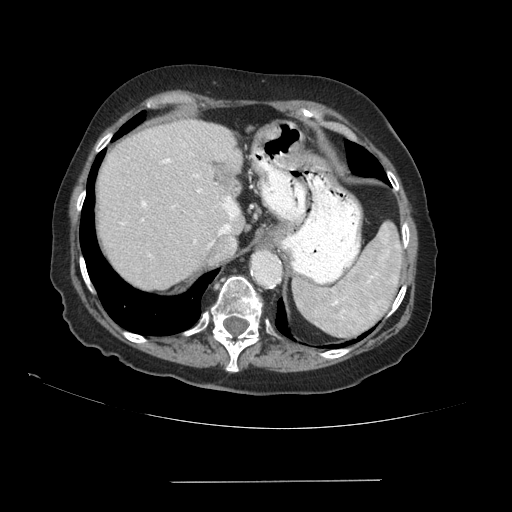
Contrast-enhanced abdominal CT (liver protocol), one axial slice. Slice 70 of 89 in the series (ordered by position). Reconstruction kernel STANDARD. 140 kVp. Soft-tissue window (W 400 / L 40 HU). 2.5 mm slice thickness. 512 × 512 image matrix, field of view 400 × 400 mm. Case-level facts recorded for this patient, not image findings: diagnosis: hepatocellular carcinoma (patient treated with transarterial chemoembolisation; whether this scan precedes or follows treatment is not stated here); TNM stage (as recorded): Stage-IVA; Child-Pugh class: A; tumour differentiation: poorly differentiated; tumour nodularity: uninodular.
Annotated regions visible in this slice (semi-automatic segmentation, software-assisted and operator-edited):
- abdominal aorta: bounding box <253,253,279,283> (left, top, right, bottom; pixels)
- liver parenchyma outside the tumour (the mass and vessels are separate outlines, so this box may not span the whole liver): <96,120,244,288>
- liver vessels: <121,159,239,246>